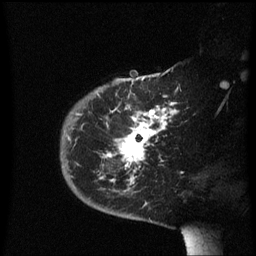
Breast MRI (dynamic contrast-enhanced), one sagittal slice. Position 44 of 60 along the scan axis. Dynamic contrast-enhanced series, image 2 of 3 at this slice position (ordered by acquisition). 1.5 T. TE 4.2 ms, TR 8.4 ms. 256 × 256 image matrix, field of view 200 × 200 mm. Patient: female, 38 years. Case-level facts recorded for this patient, not image findings: setting: breast cancer imaged before/during neoadjuvant chemotherapy; receptor status: HER2-positive.
Outlined on this slice (semi-automatic segmentation, software-assisted and operator-edited):
- analysis volume of interest (the breast-tissue region the enhancement analysis was run in; not a lesion): bounding box (x1, y1, x2, y2) in pixels: (60, 78, 179, 213)
- tumour enhancement mask (voxels above the 70 % enhancement threshold inside the analysis volume of interest): (103, 102, 179, 185)